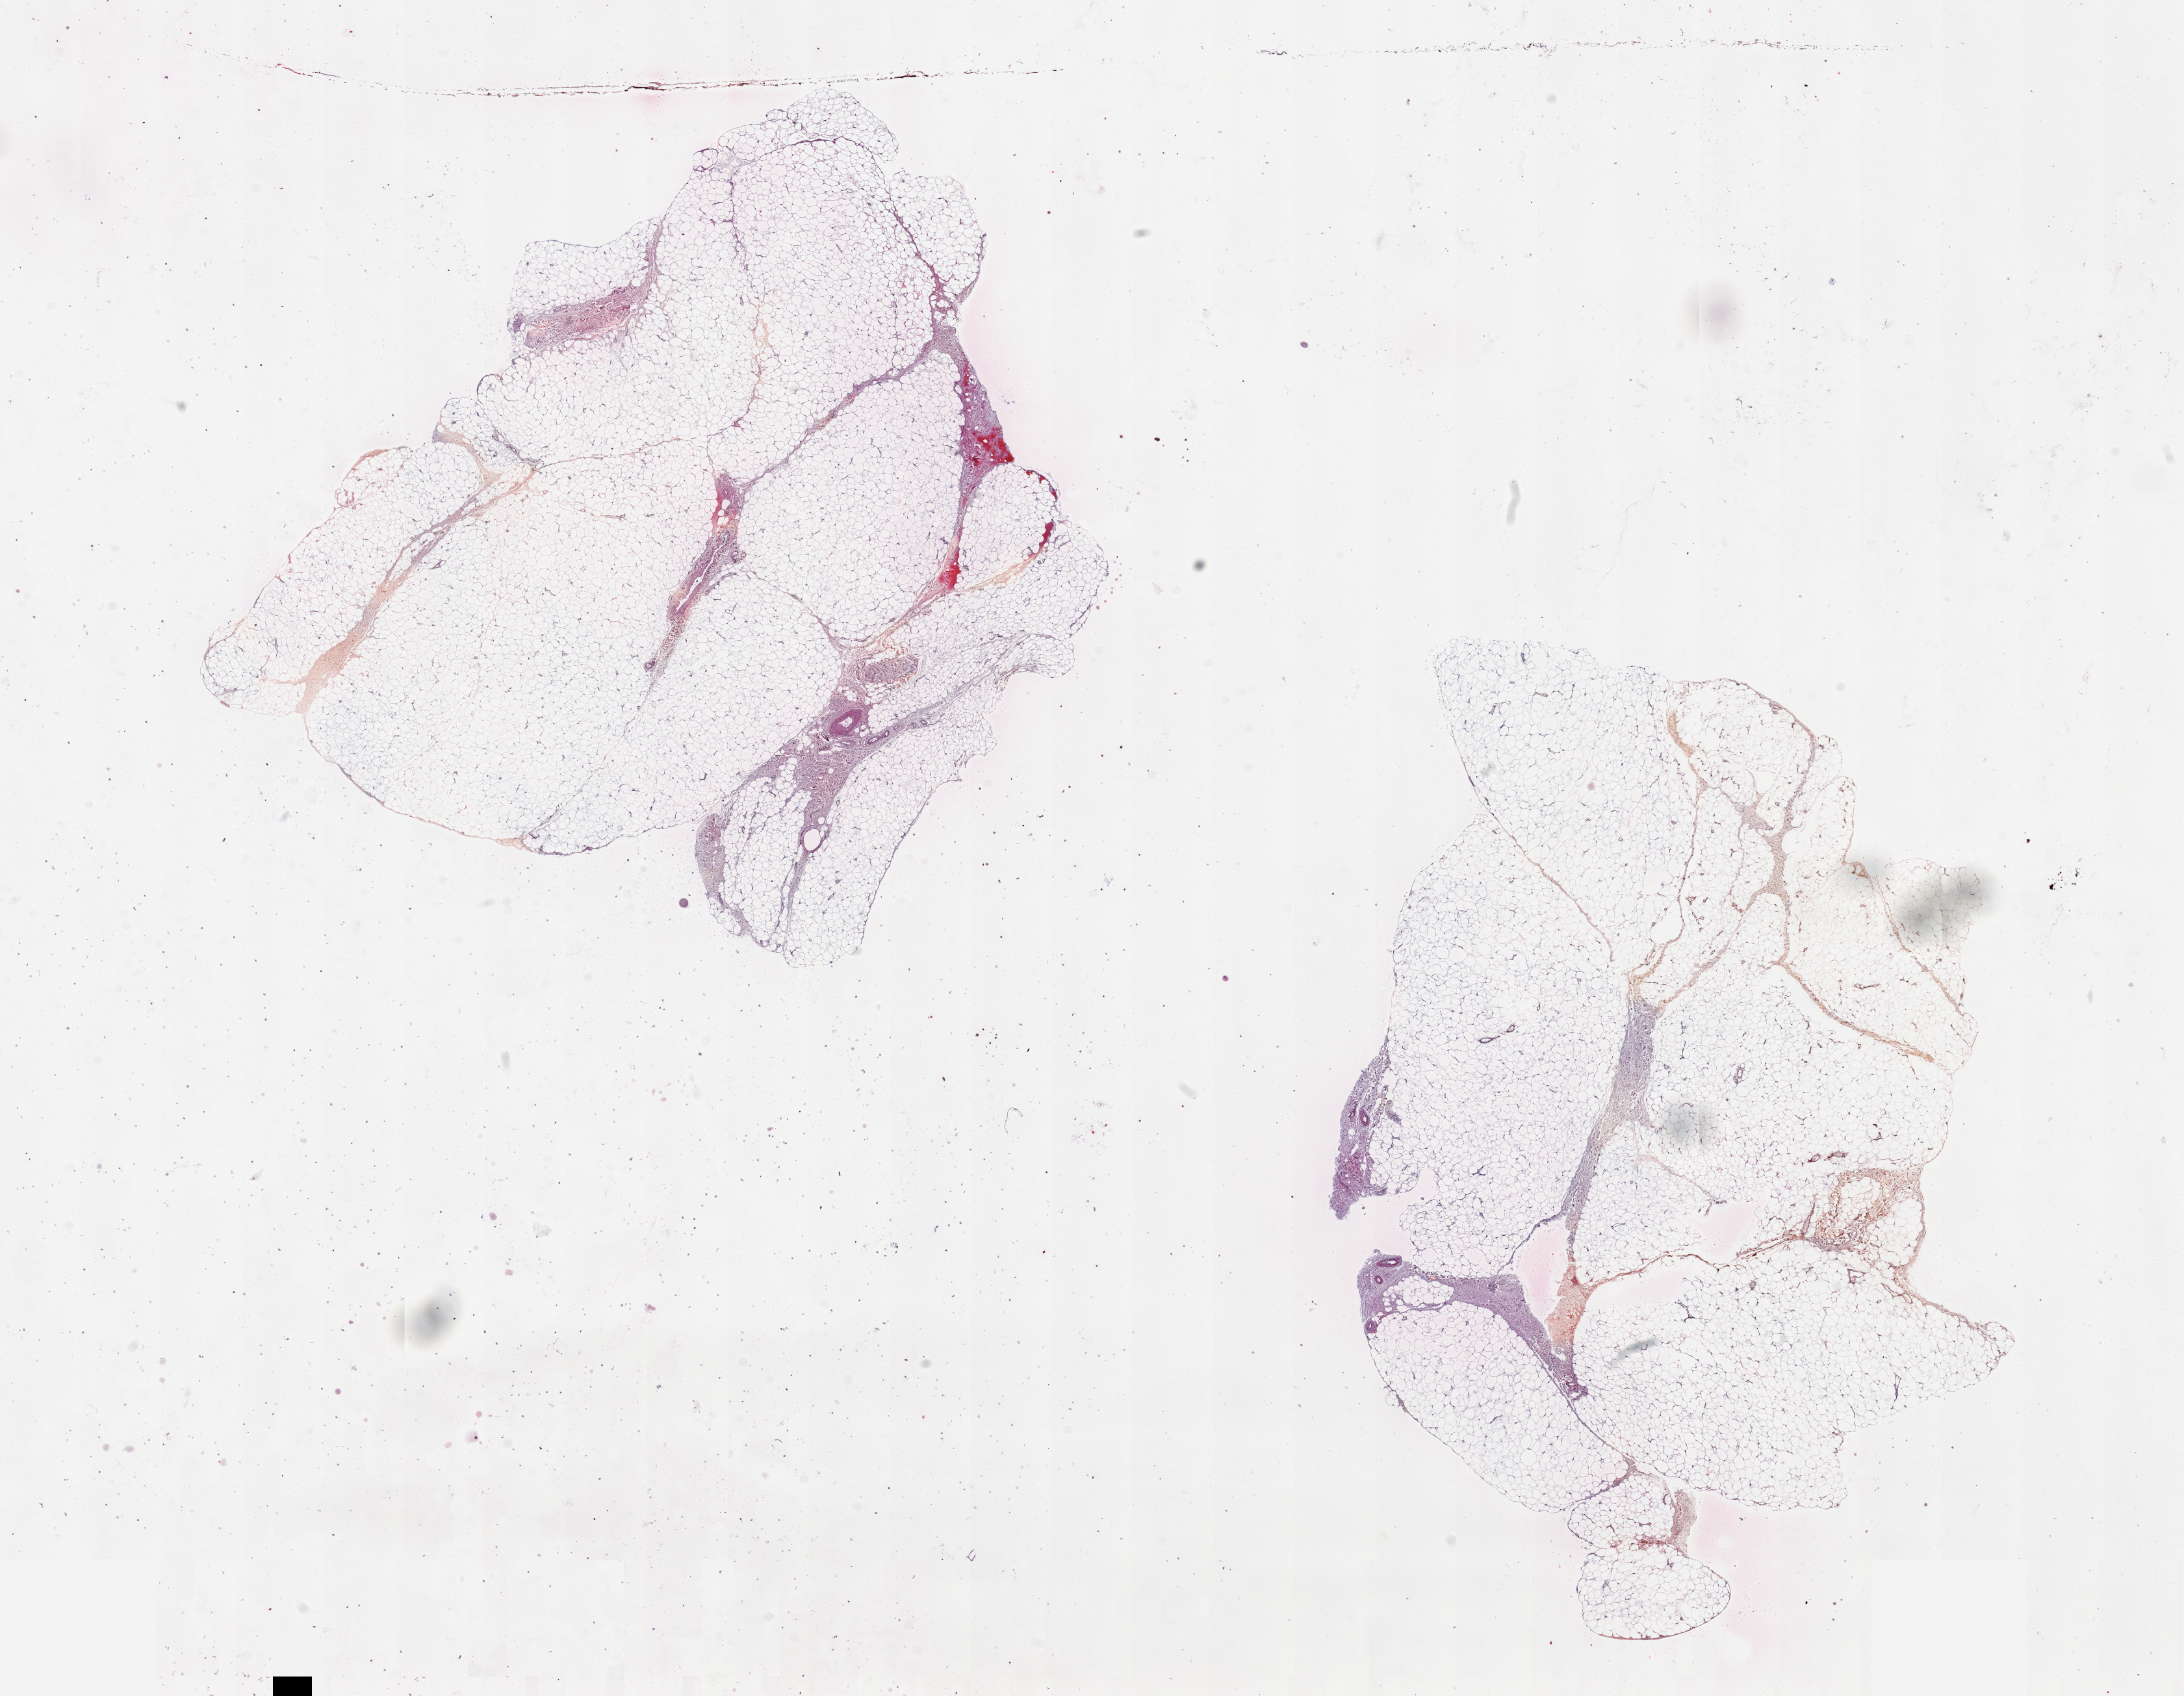
Whole-slide image, H&E stain, whole scanned area (about 26.6 x 20.6 mm, acquisition: 20x scan) shown as a low-resolution overview; PAXgene-fixed paraffin-embedded (PFPE) section; target tissue: adipose tissue; tissue donor sample. Female donor.
Review note (as recorded): 2 pieces, 11x8 & 12x8mm; Small artefactual holes.